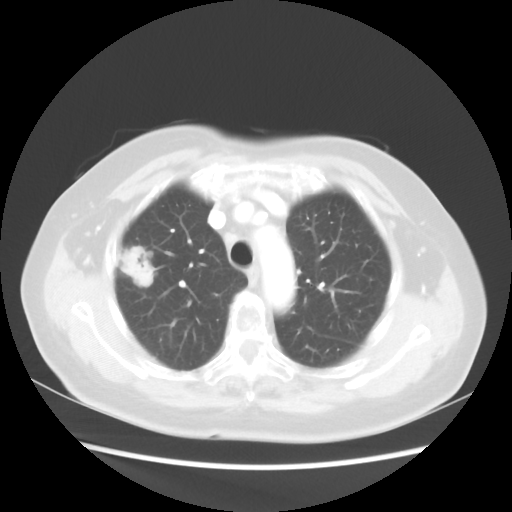
Chest CT, one axial slice; slice 36 of 48 in the series (ordered by position); reconstruction kernel STANDARD; lung window (W 1500 / L -600 HU); 5 mm slice thickness; 512 × 512 image matrix. Patient: female, 75 years. Case-level facts recorded for this patient, not image findings: clinical TNM (as recorded): T1c N0 M0.
Structures marked on this image (rectangle marked by the reading radiologist):
- lung tumour (recorded histology: adenocarcinoma): bounding box <116,240,157,293> (left, top, right, bottom; pixels)